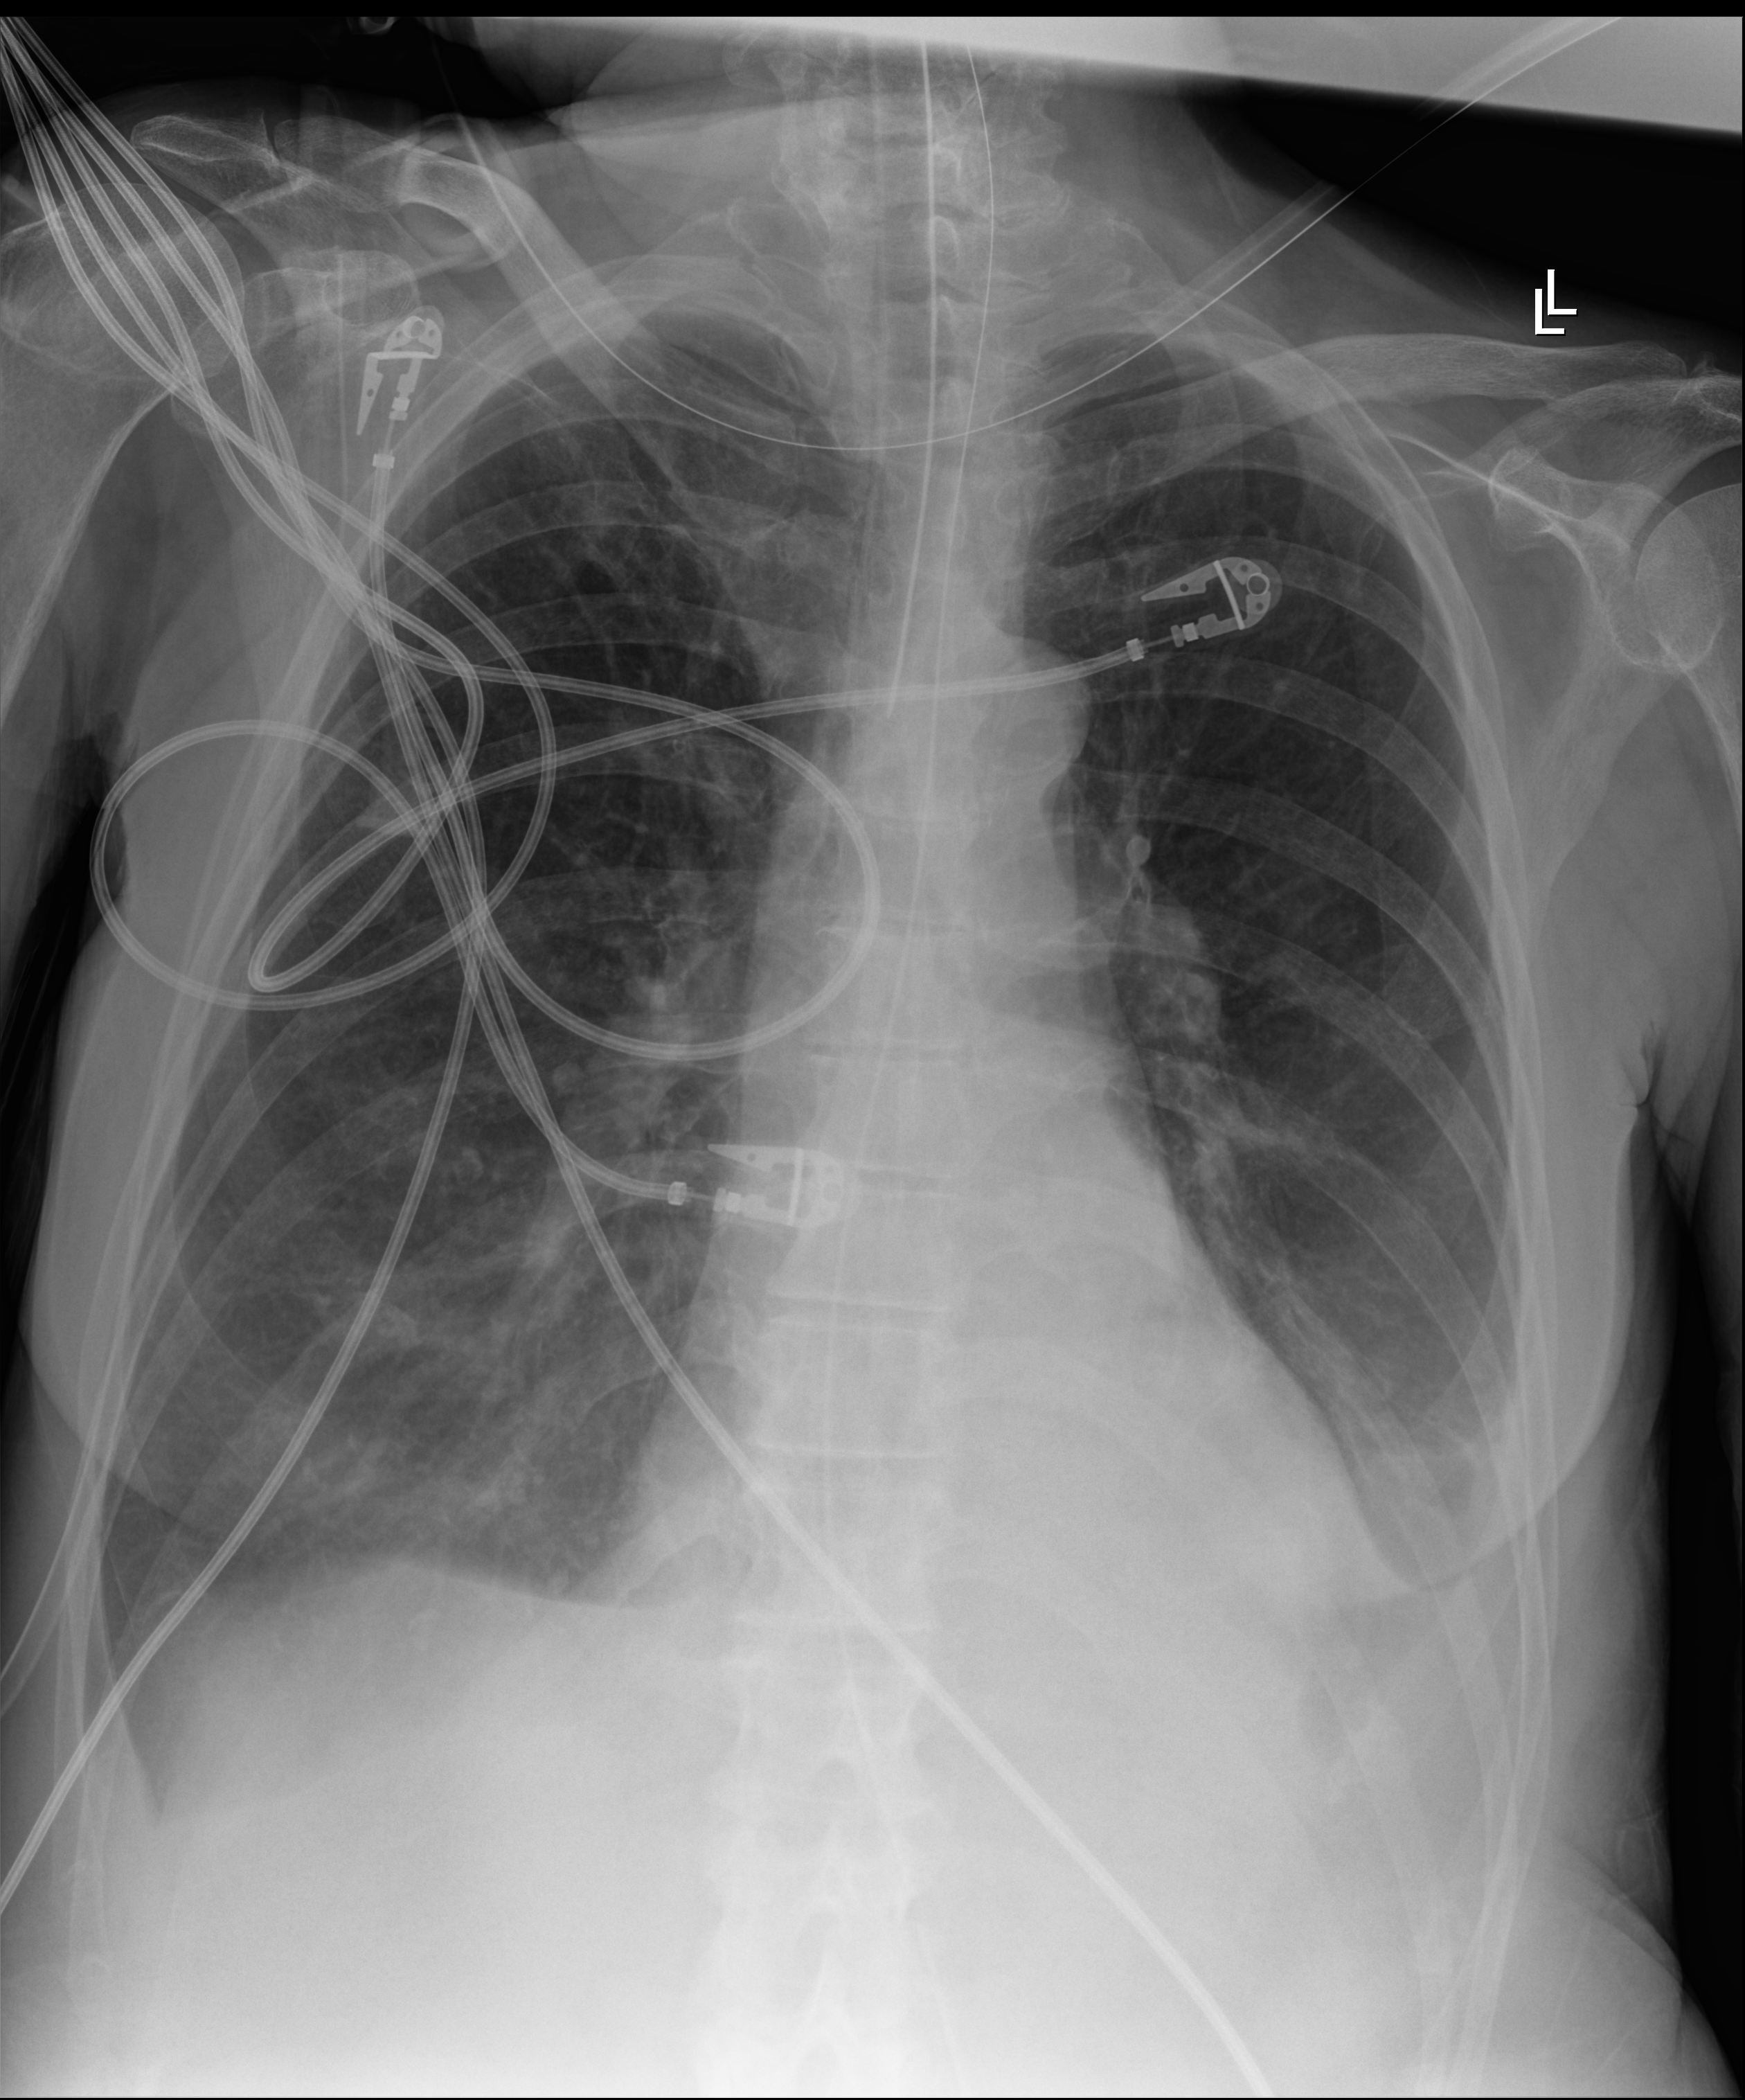
Chest radiograph; anteroposterior (AP) projection. Female patient hospitalised with COVID-19, age 60–74 years.
From the hospital-stay record, not from the radiograph (when in the stay this image was taken is not recorded): mechanically ventilated during this hospital stay: yes; admitted to intensive care during this hospital stay: yes; length of hospital stay: 38 days.